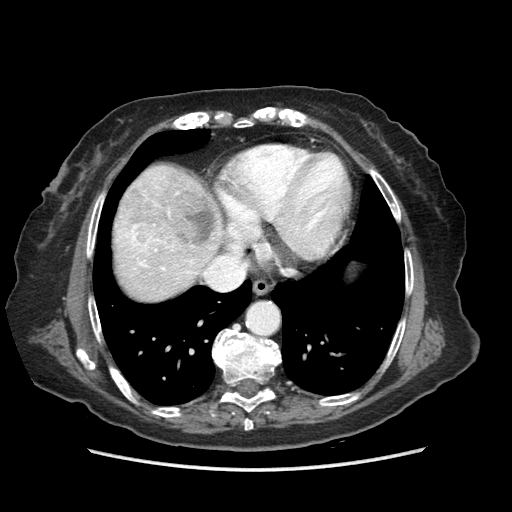
Contrast-enhanced abdominal CT (liver protocol), one axial slice; position 76 of 89 along the scan axis; 140 kVp; soft-tissue window (W 400 / L 40 HU); 2.5 mm slice thickness; 512 × 512 image matrix, field of view 360 × 360 mm. Case-level facts recorded for this patient, not image findings: diagnosis: hepatocellular carcinoma (patient treated with transarterial chemoembolisation; whether this scan precedes or follows treatment is not stated here); TNM stage (as recorded): Stage-IIIA; Child-Pugh class: A; tumour differentiation: well differentiated; tumour nodularity: multinodular.
Outlined on this slice (semi-automatically segmented with operator editing):
- liver parenchyma outside the tumour (the mass and vessels are separate outlines, so this box may not span the whole liver): bounding box (x1, y1, x2, y2) in pixels: (114, 164, 356, 300)
- mass: (161, 190, 214, 245)
- liver vessels: (124, 187, 196, 274)